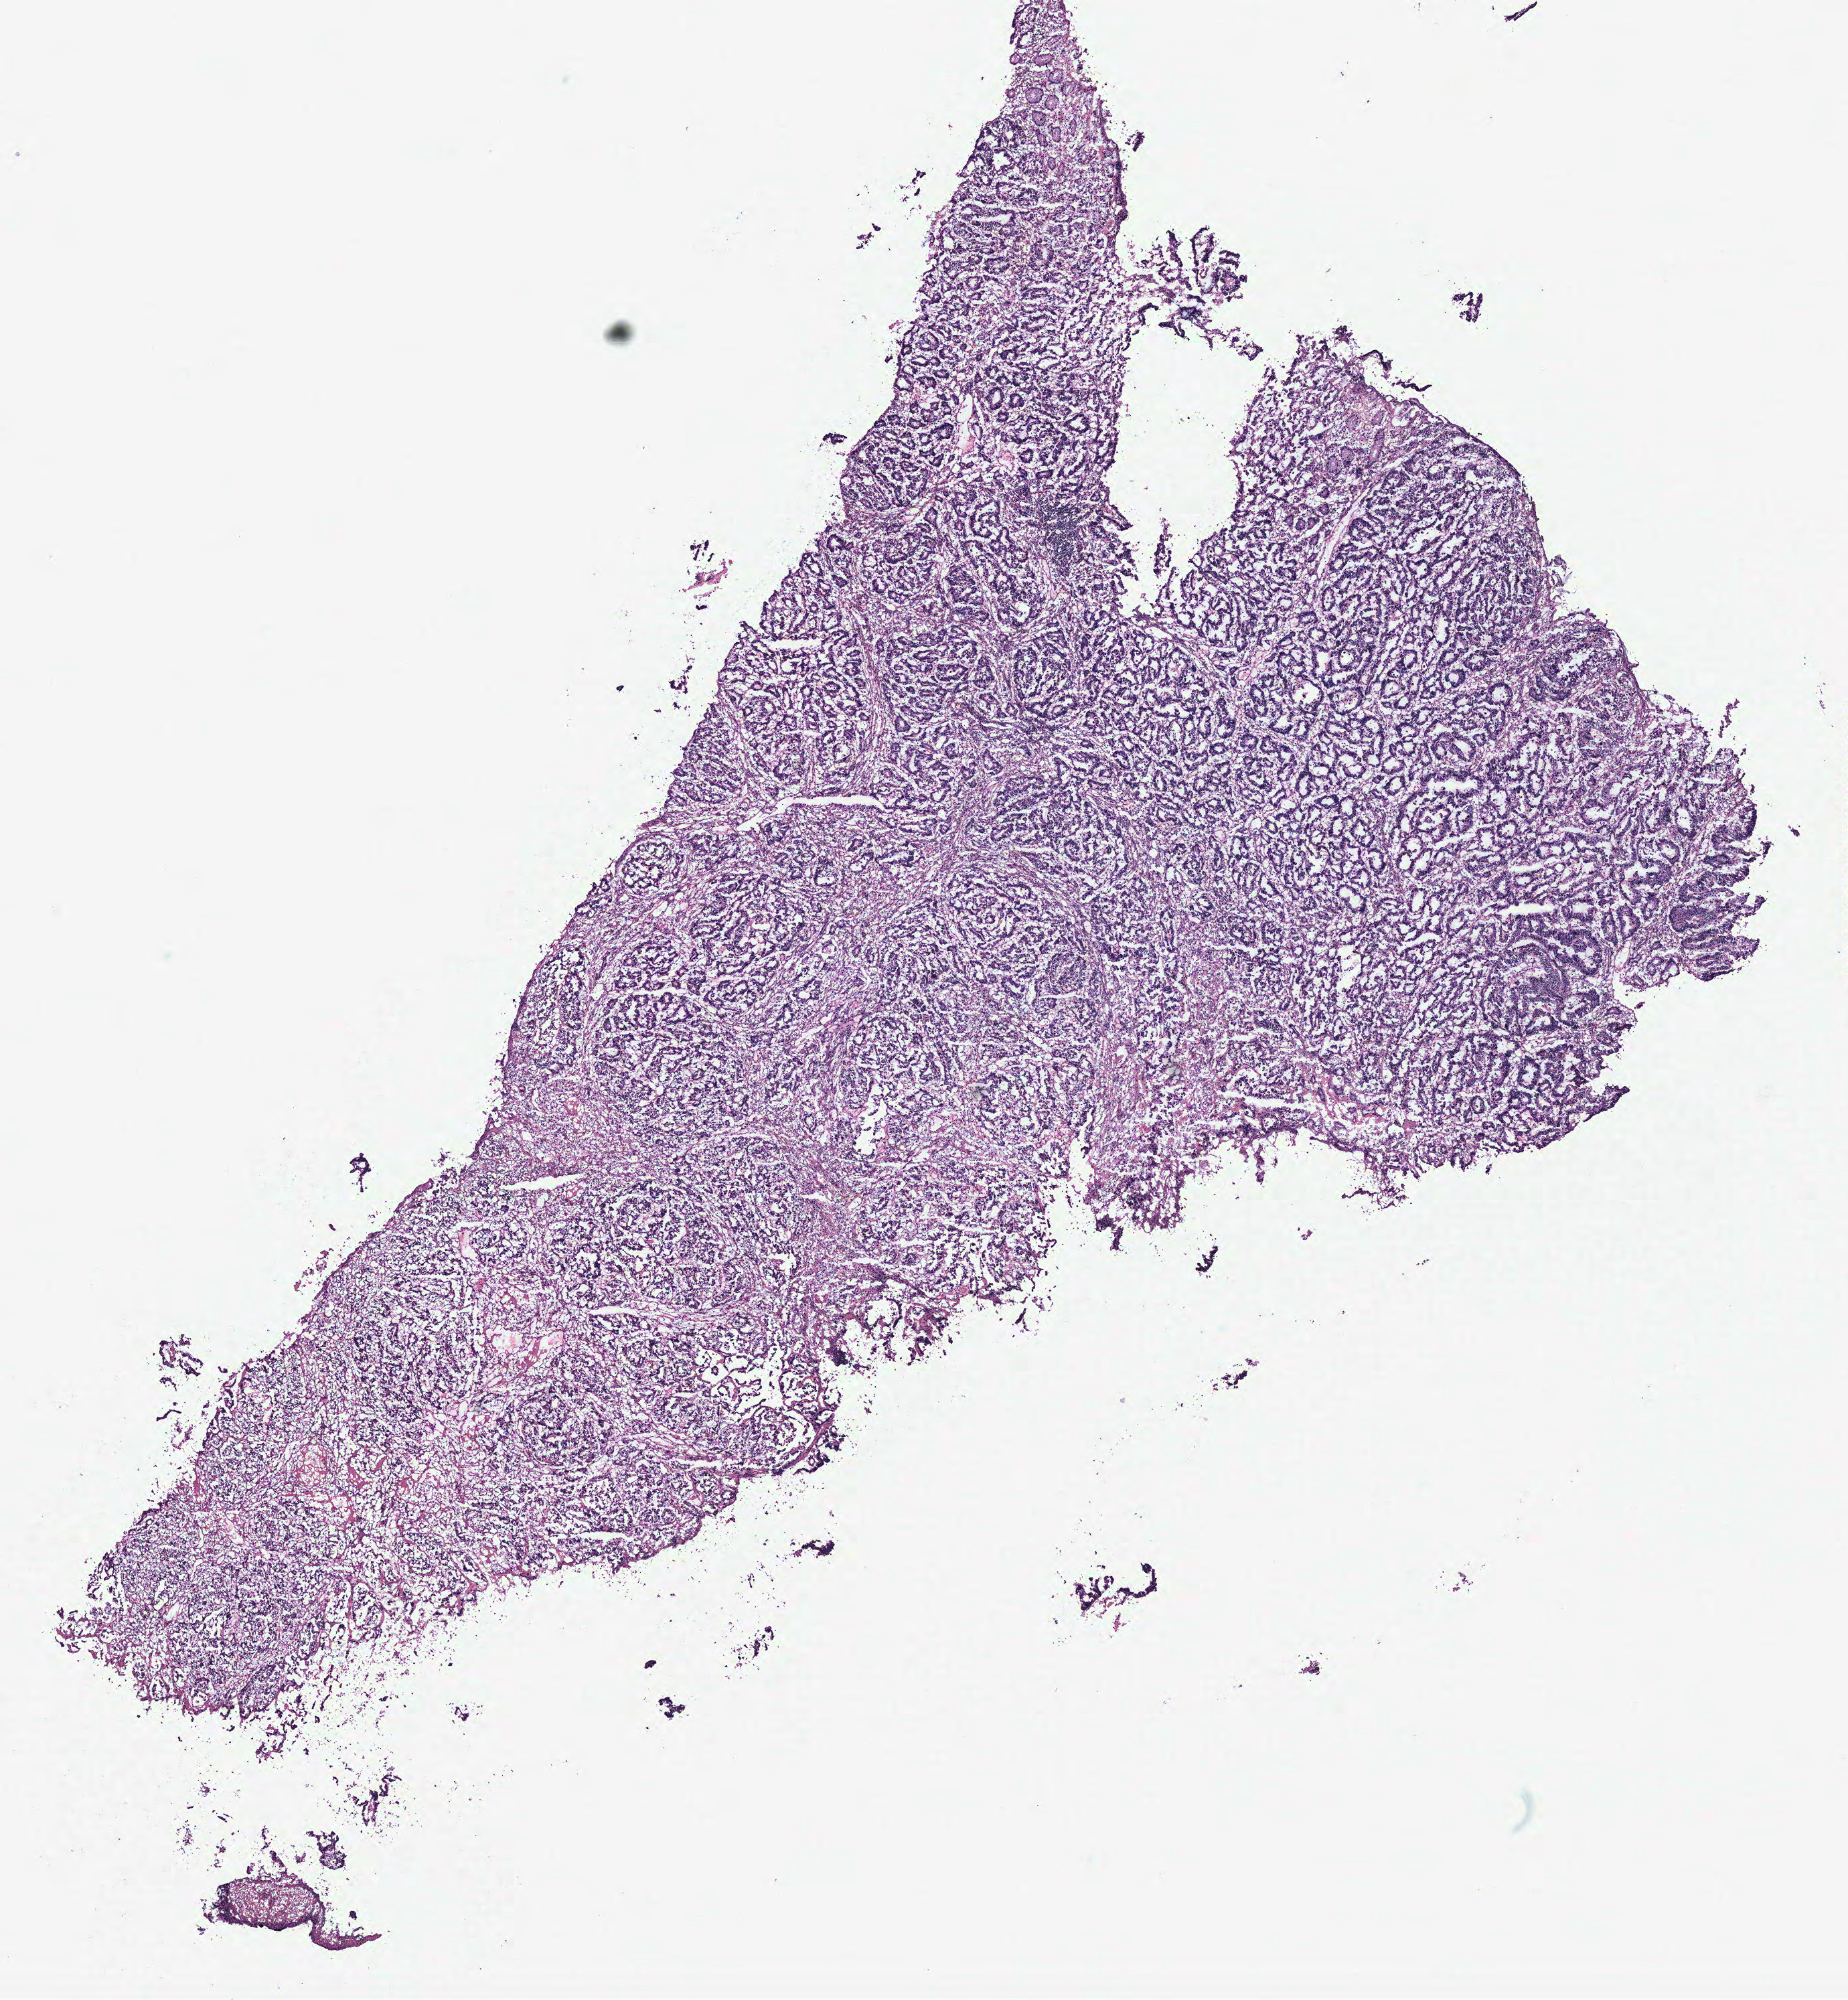
Whole-slide histology image, H&E-stained, whole scanned area (about 11.0 x 12.0 mm) shown as a low-resolution overview, colon, tumour tissue. Patient: male, age 50 years.
- AJCC pathologic stage: IV
- primary tumour site (as recorded): colon
- diagnosis: Adenocarcinoma, NOS